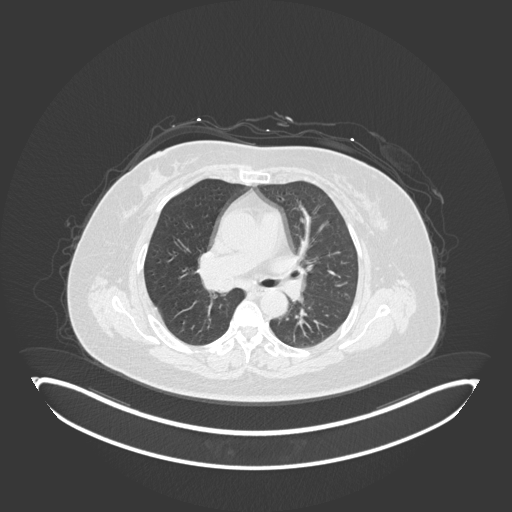
Chest CT, one axial slice; position 96 of 245 along the scan axis; 120 kVp; lung window (W 1500 / L -600 HU); 1 mm slice thickness; 512 × 512 image matrix, field of view 500 × 500 mm. Female patient, age 60 years. From the clinical record (not read from this slice): clinical TNM (as recorded): T1c N0 M0; histopathological grade: G1-G2.
Annotated regions visible in this slice (rectangle marked by the reading radiologist):
- lung tumour (recorded histology: squamous cell carcinoma): bounding box [x1, y1, x2, y2] px = [200, 271, 237, 294]